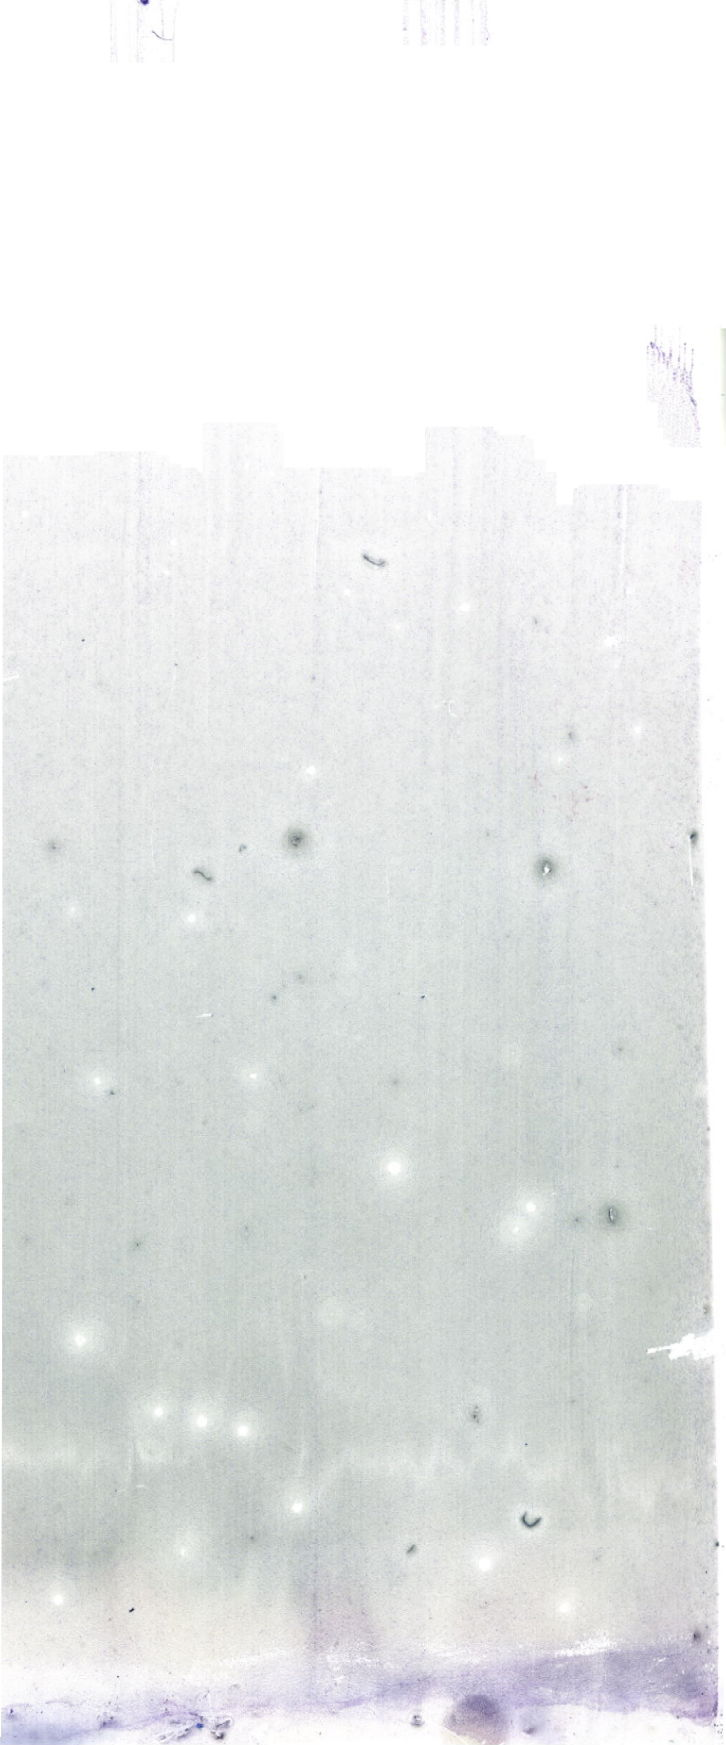
May-Grünwald–Giemsa-stained marrow aspirate smear (whole slide) — whole scanned area (about 20.6 x 49.5 mm) shown as a low-resolution overview. Male patient.
Diagnosis: Blast Phase Chronic Myeloid Leukemia, BCR-ABL1 Positive.